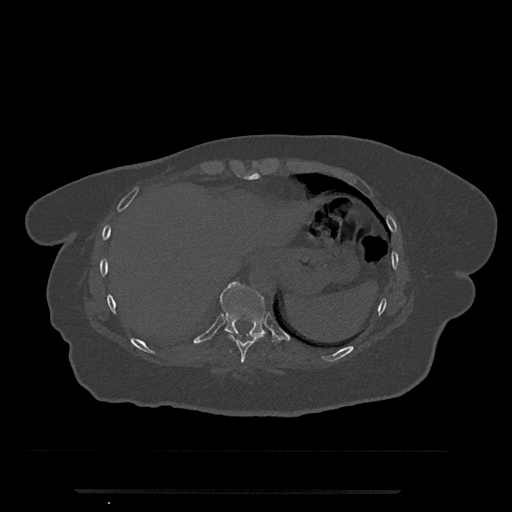
CT including the spine, one axial slice; slice 312 of 797 in the series (ordered by position); reconstruction kernel Br40s/3; bone window (W 1800 / L 400 HU); 0.5 mm slice thickness; 512 × 512 image matrix, field of view 440 × 440 mm. Patient: female, 51 years. Case-level facts recorded for this patient, not image findings: primary cancer: neuro; vertebrae with lytic lesions (as recorded): T8.
Outlined on this slice (semi-automatically segmented with operator editing):
- T10 vertebra: box from (x=219, y=281) to (x=267, y=337) px
- T9 vertebra: (x=228, y=334)–(x=265, y=363)